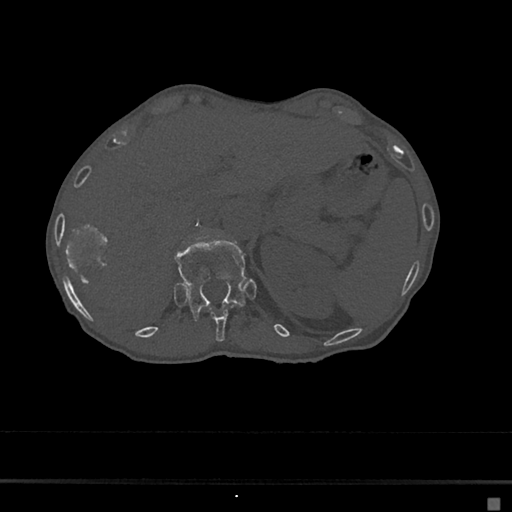
CT including the spine, one axial slice; position 135 of 797 along the scan axis; reconstruction kernel Br40s/3; 120 kVp; bone window (W 1800 / L 400 HU); 0.5 mm slice thickness; 512 × 512 image matrix. Female patient, age 68 years. From the clinical record (not read from this slice): primary cancer: renal.
Annotated regions visible in this slice (semi-automatically segmented with operator editing):
- T11 vertebra: bounding box (x1, y1, x2, y2) in pixels: (211, 310, 230, 342)
- T12 vertebra: (175, 238, 248, 319)